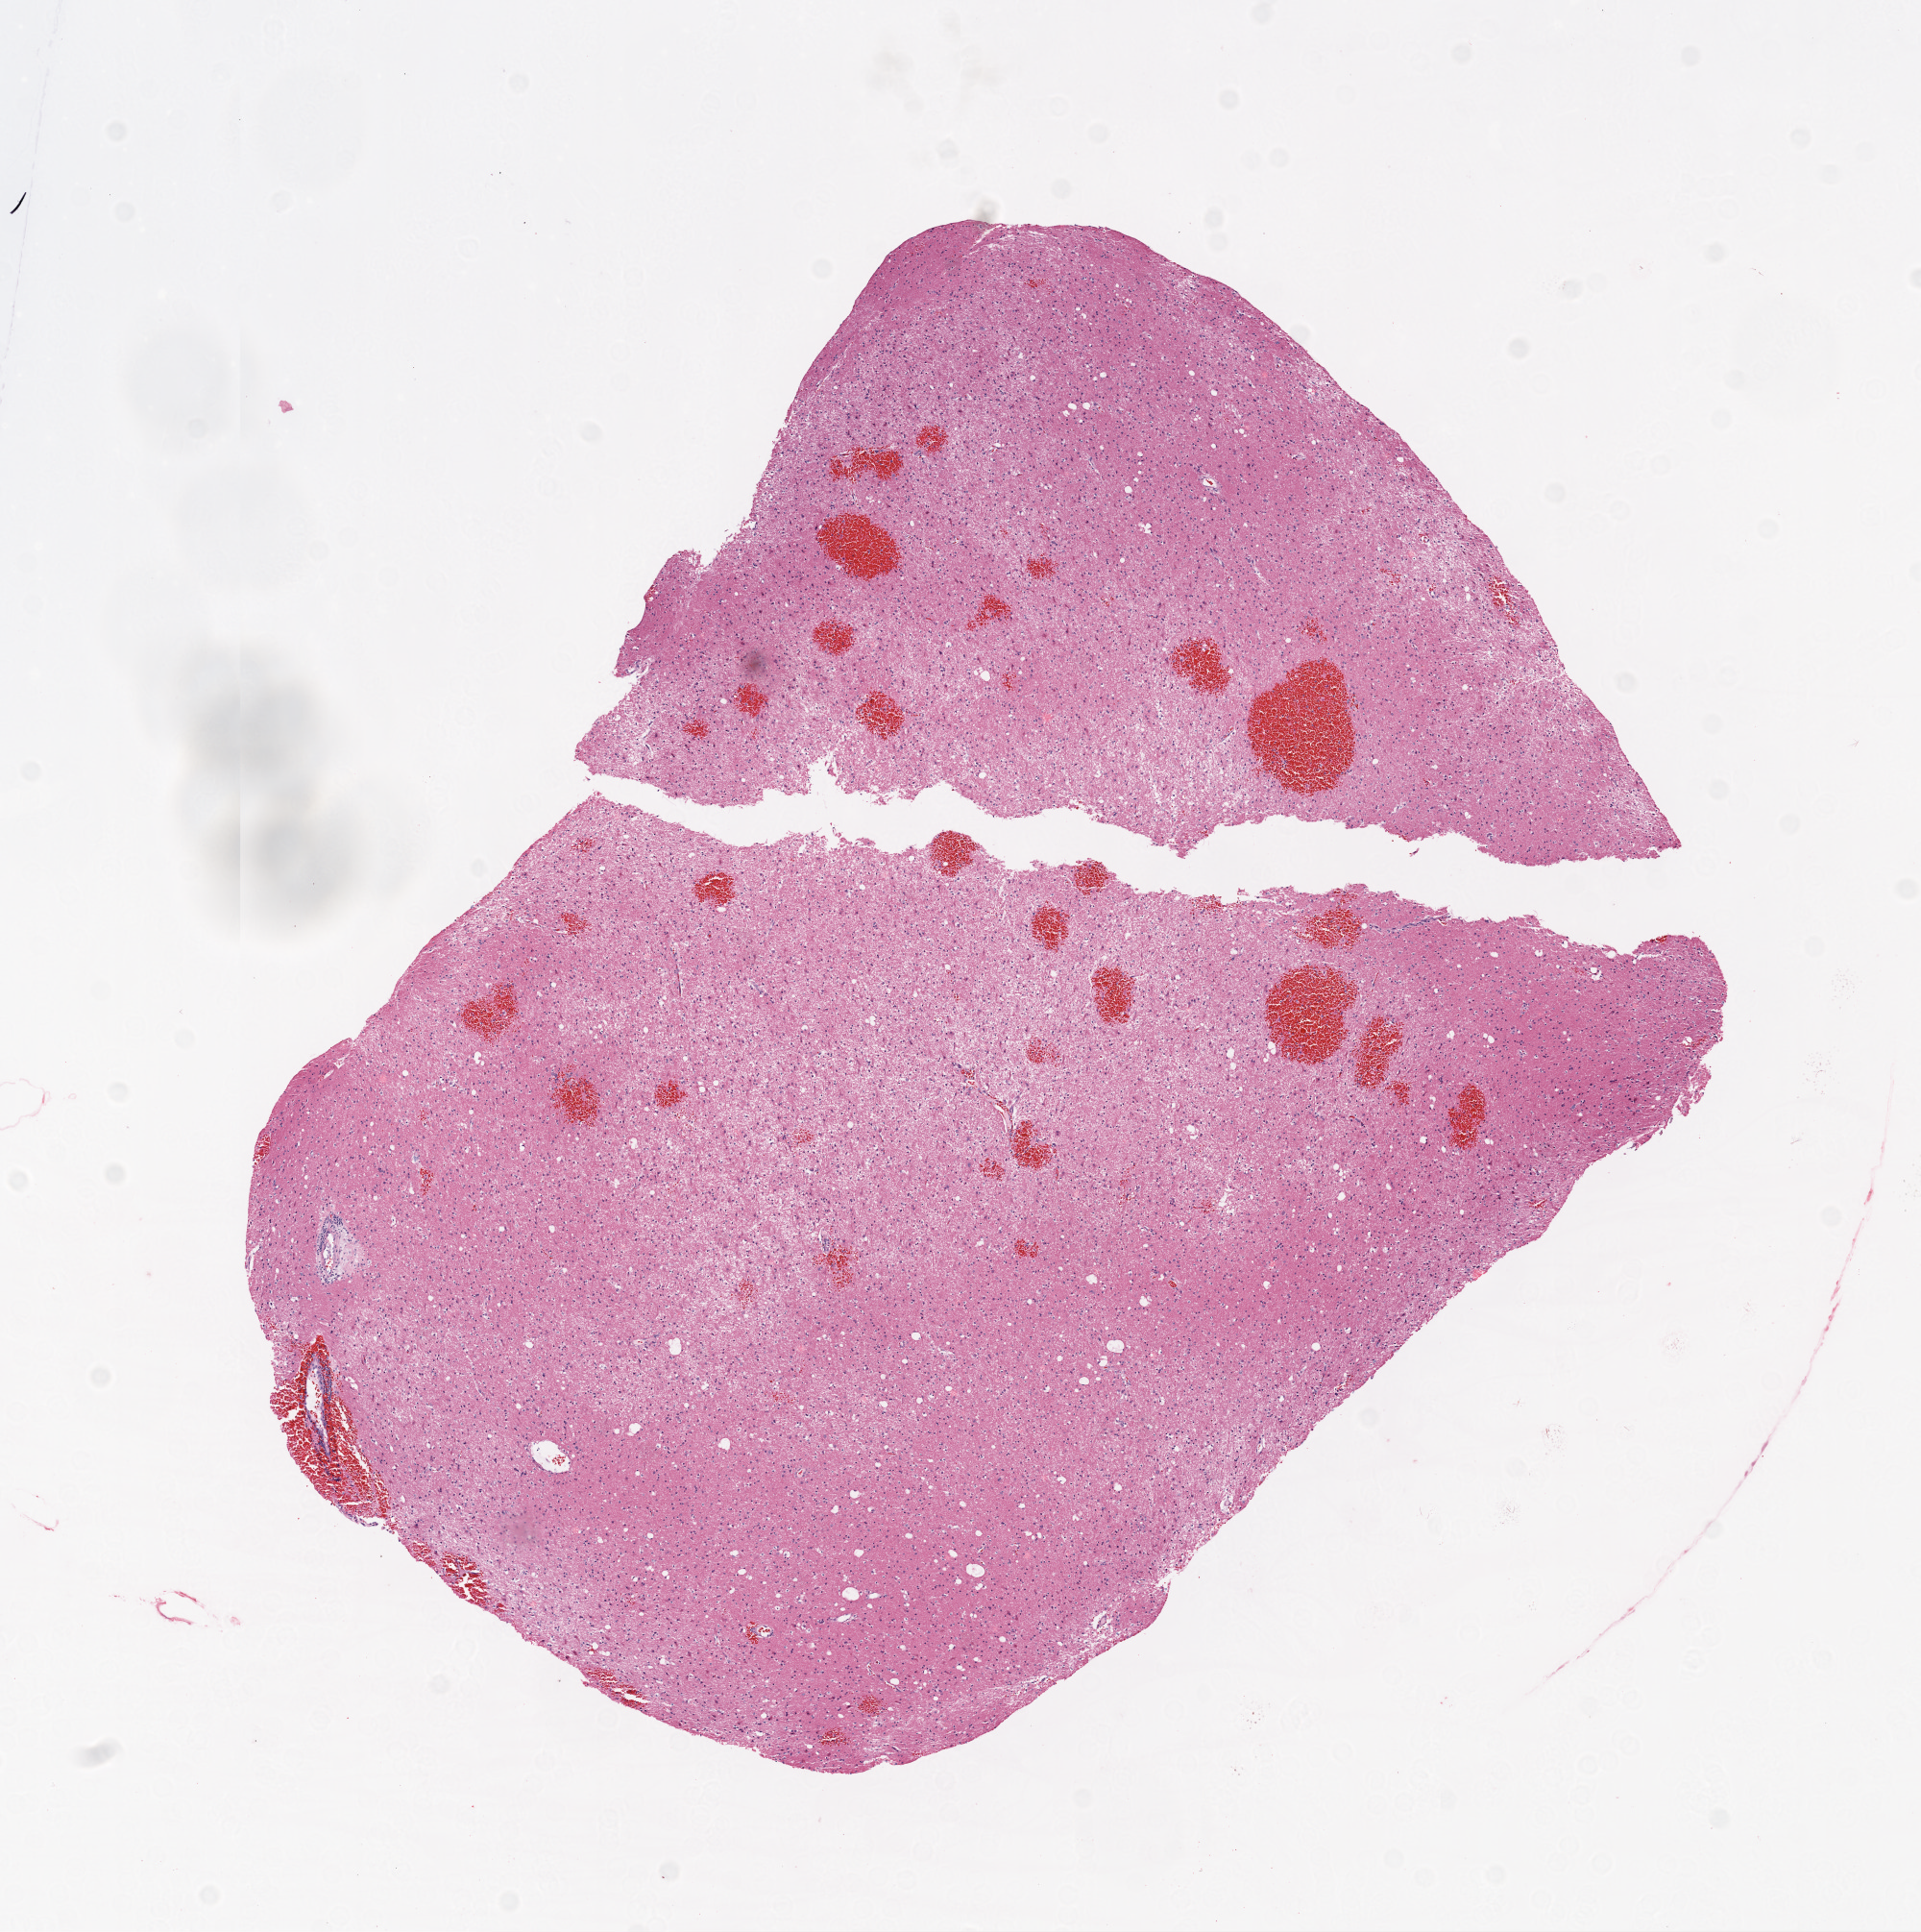
Whole-slide histology image, H&E-stained, a low-resolution overview of the entire scanned area, about 8.0 x 8.1 mm; formalin-fixed paraffin-embedded (FFPE) diagnostic section; primary tumour sample from the brain. Male patient; age at initial diagnosis 61 years.
Diagnosis: Glioblastoma.